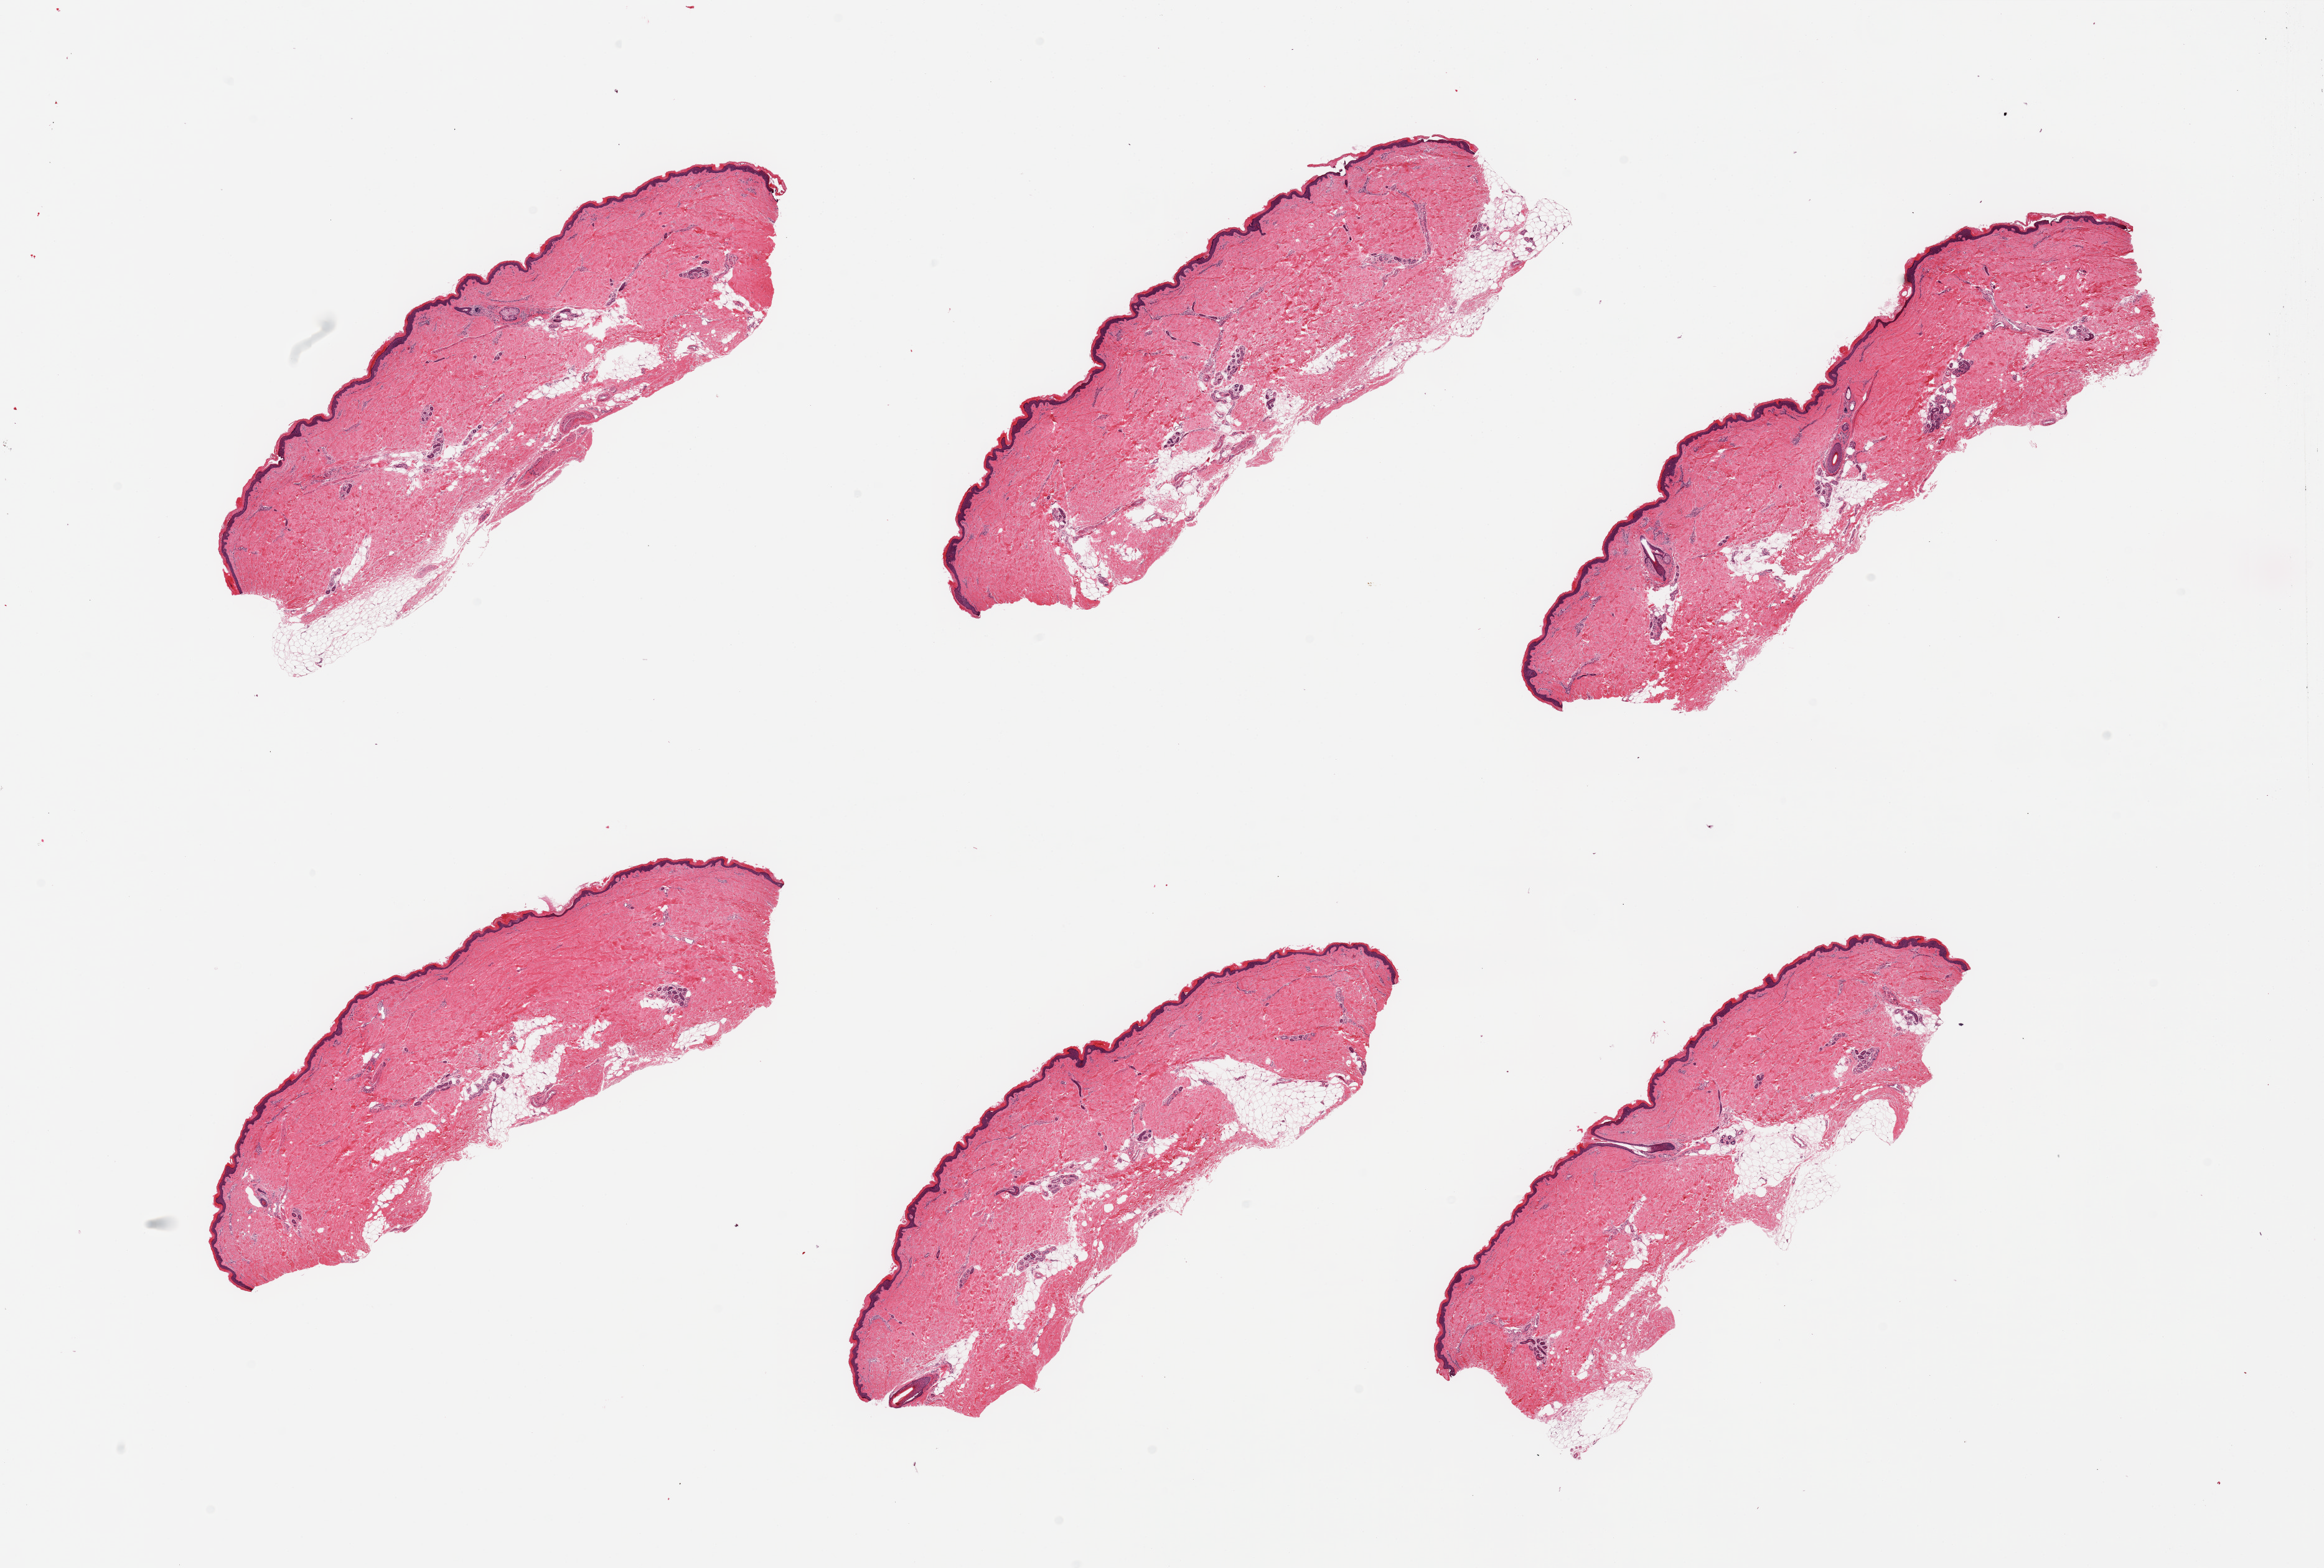
H&E whole-slide image, brightfield — shown as a low-resolution overview of the whole scanned area (about 29.5 x 19.9 mm, acquisition: 20x scan); PAXgene-fixed paraffin-embedded (PFPE) section; sampled site (target tissue): skin of lower leg; donor tissue sample. Donor sex: male.
Pathologist's review note for this sample: 6 pieces; 10-20% internal/external fat, squamous epithelium measures 45 microns thick.